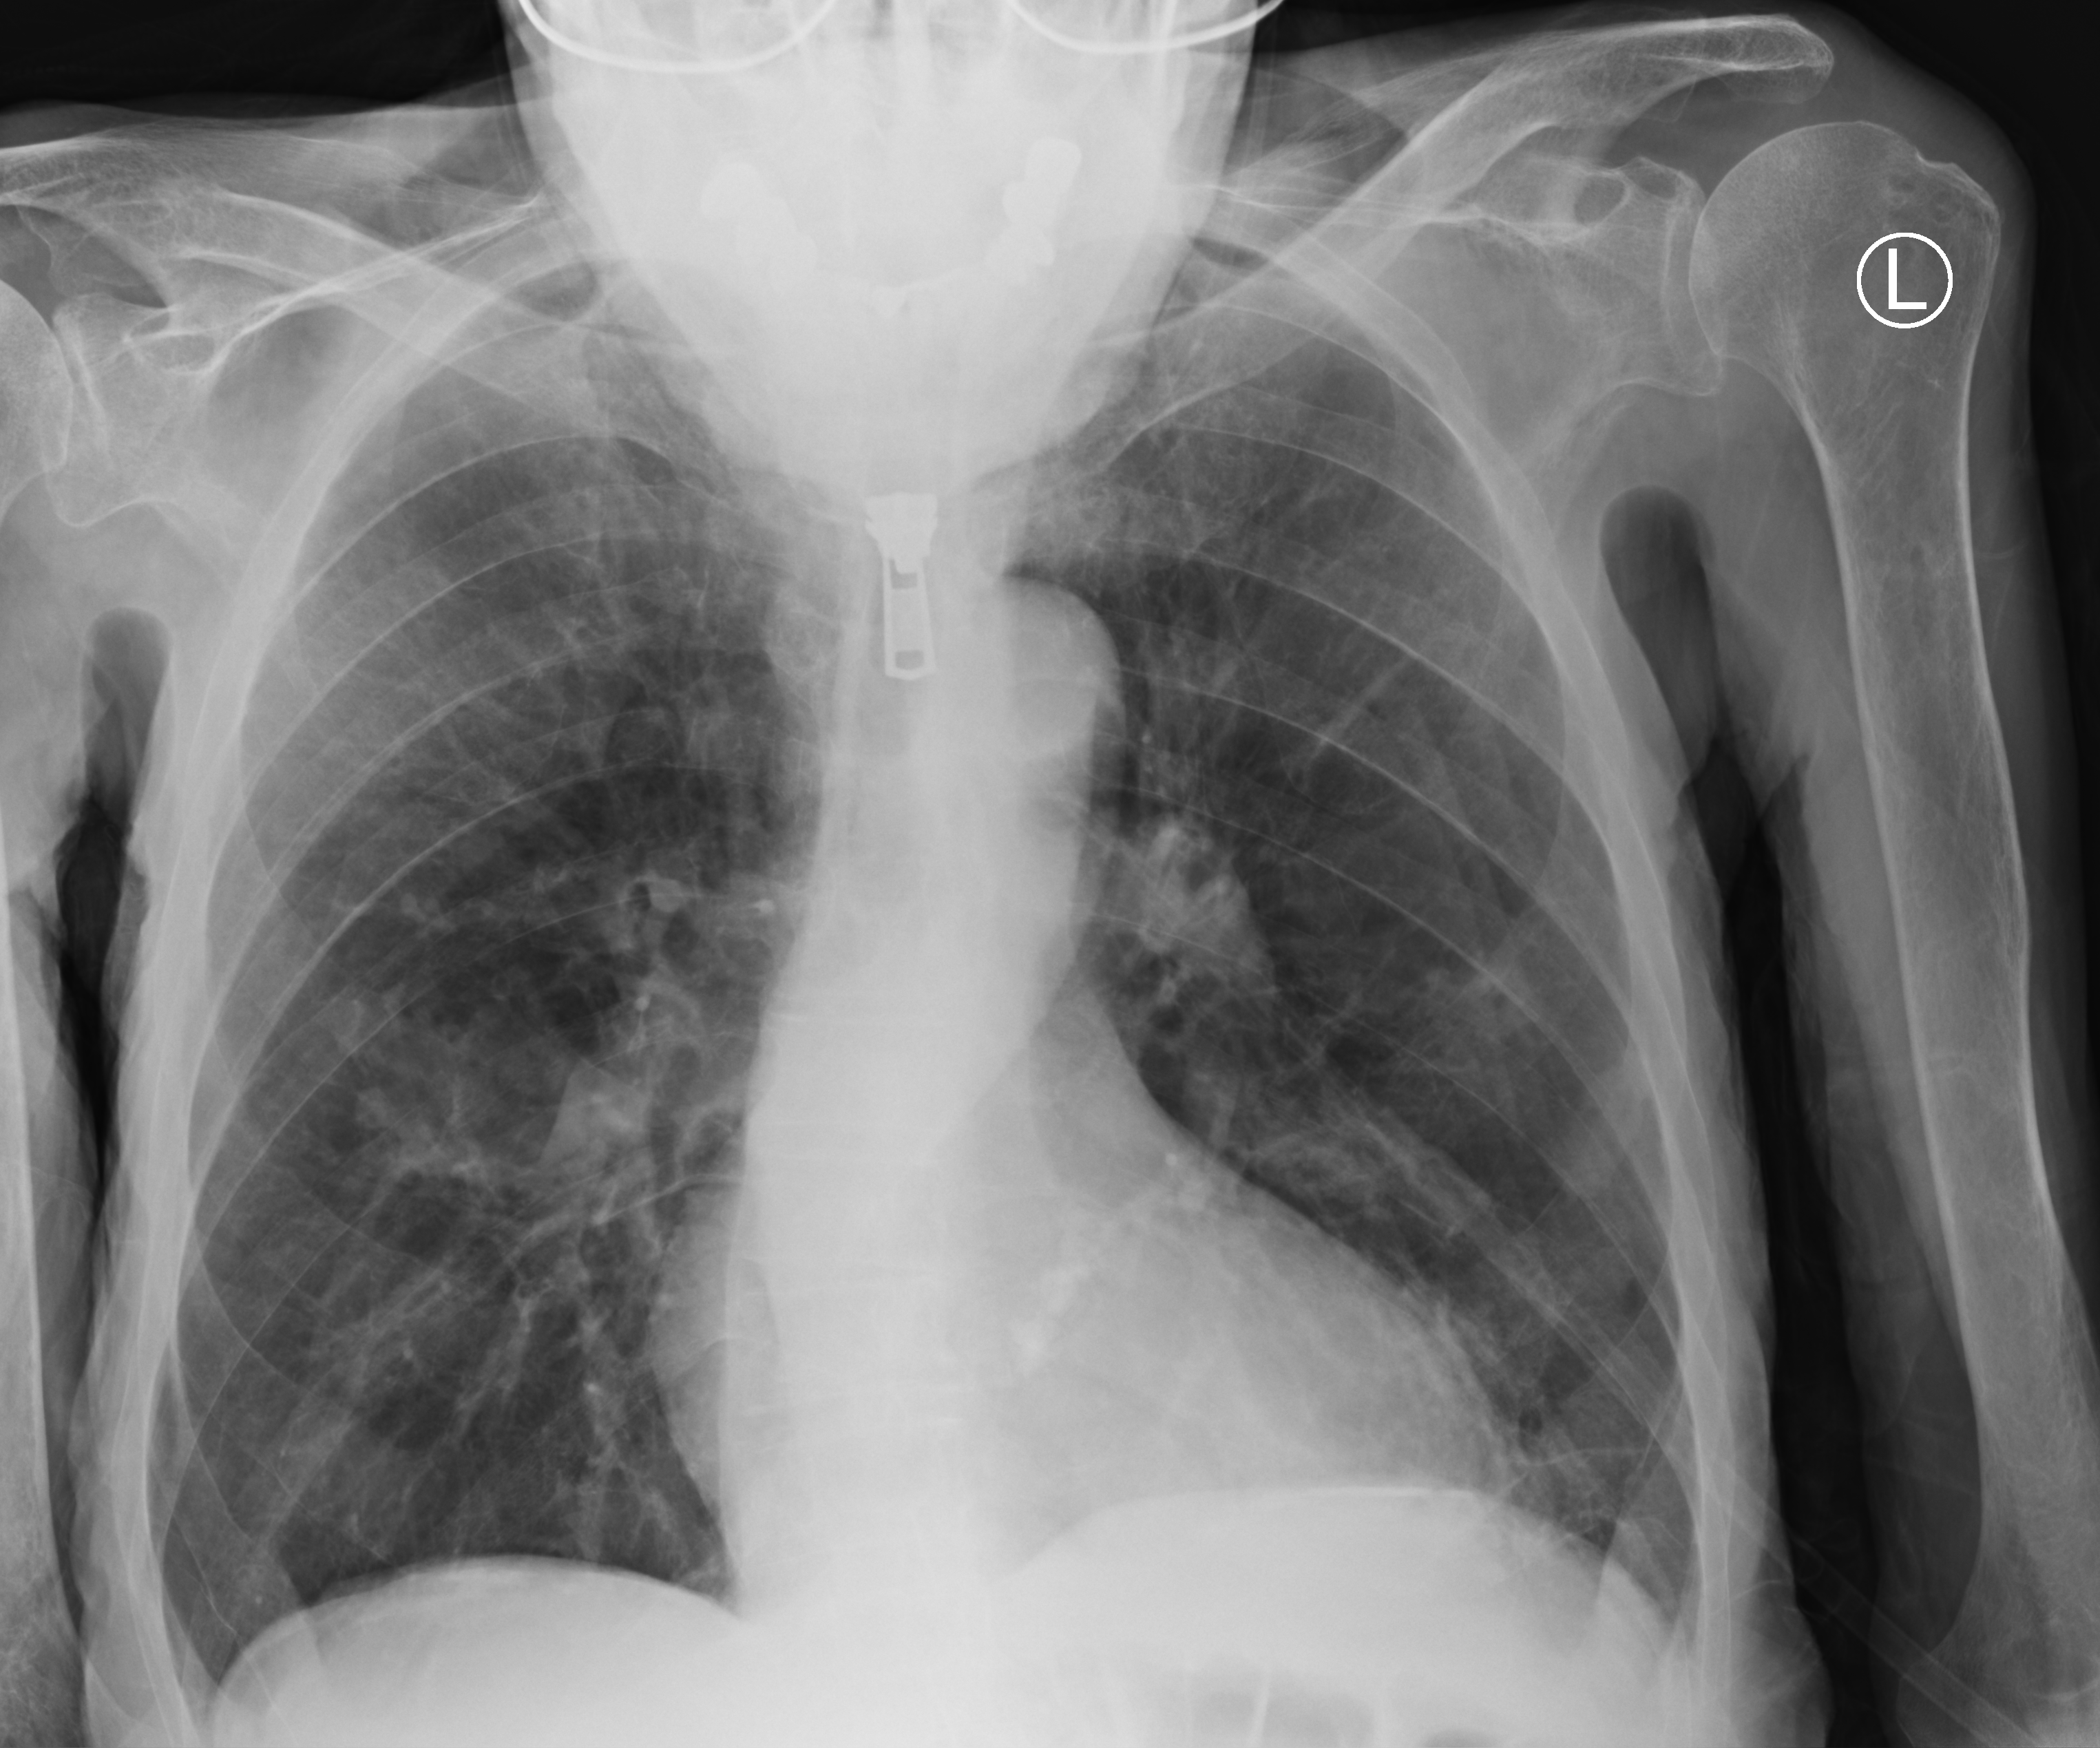
Portable chest radiograph. Male patient hospitalised with COVID-19, age 75–90 years.
Hospital-stay facts (about this admission, not read from this image; timing relative to this image not recorded): mechanically ventilated during this hospital stay: no.